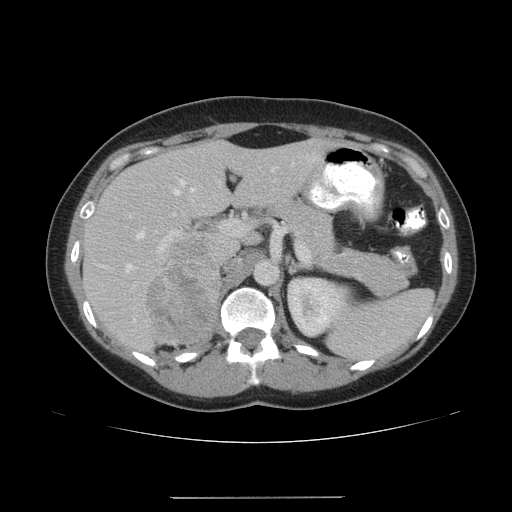
Contrast-enhanced abdominal CT, one axial slice. Slice 113 of 161 in the series (ordered by position). Reconstruction kernel STANDARD. 120 kVp. Intravenous contrast given. Soft-tissue window (W 400 / L 40 HU). 512 × 512 image matrix, field of view 380 × 380 mm. Female patient. From the clinical record (not read from this slice): diagnosis: adrenocortical carcinoma; tumour side: right adrenal; tumour size at pathology: 9 cm; Ki-67 index: 14 %; stage (as recorded): 3.
Structures marked on this image (semi-automatically segmented with operator editing):
- mass: bounding box (x1, y1, x2, y2) in pixels: (149, 242, 218, 343)